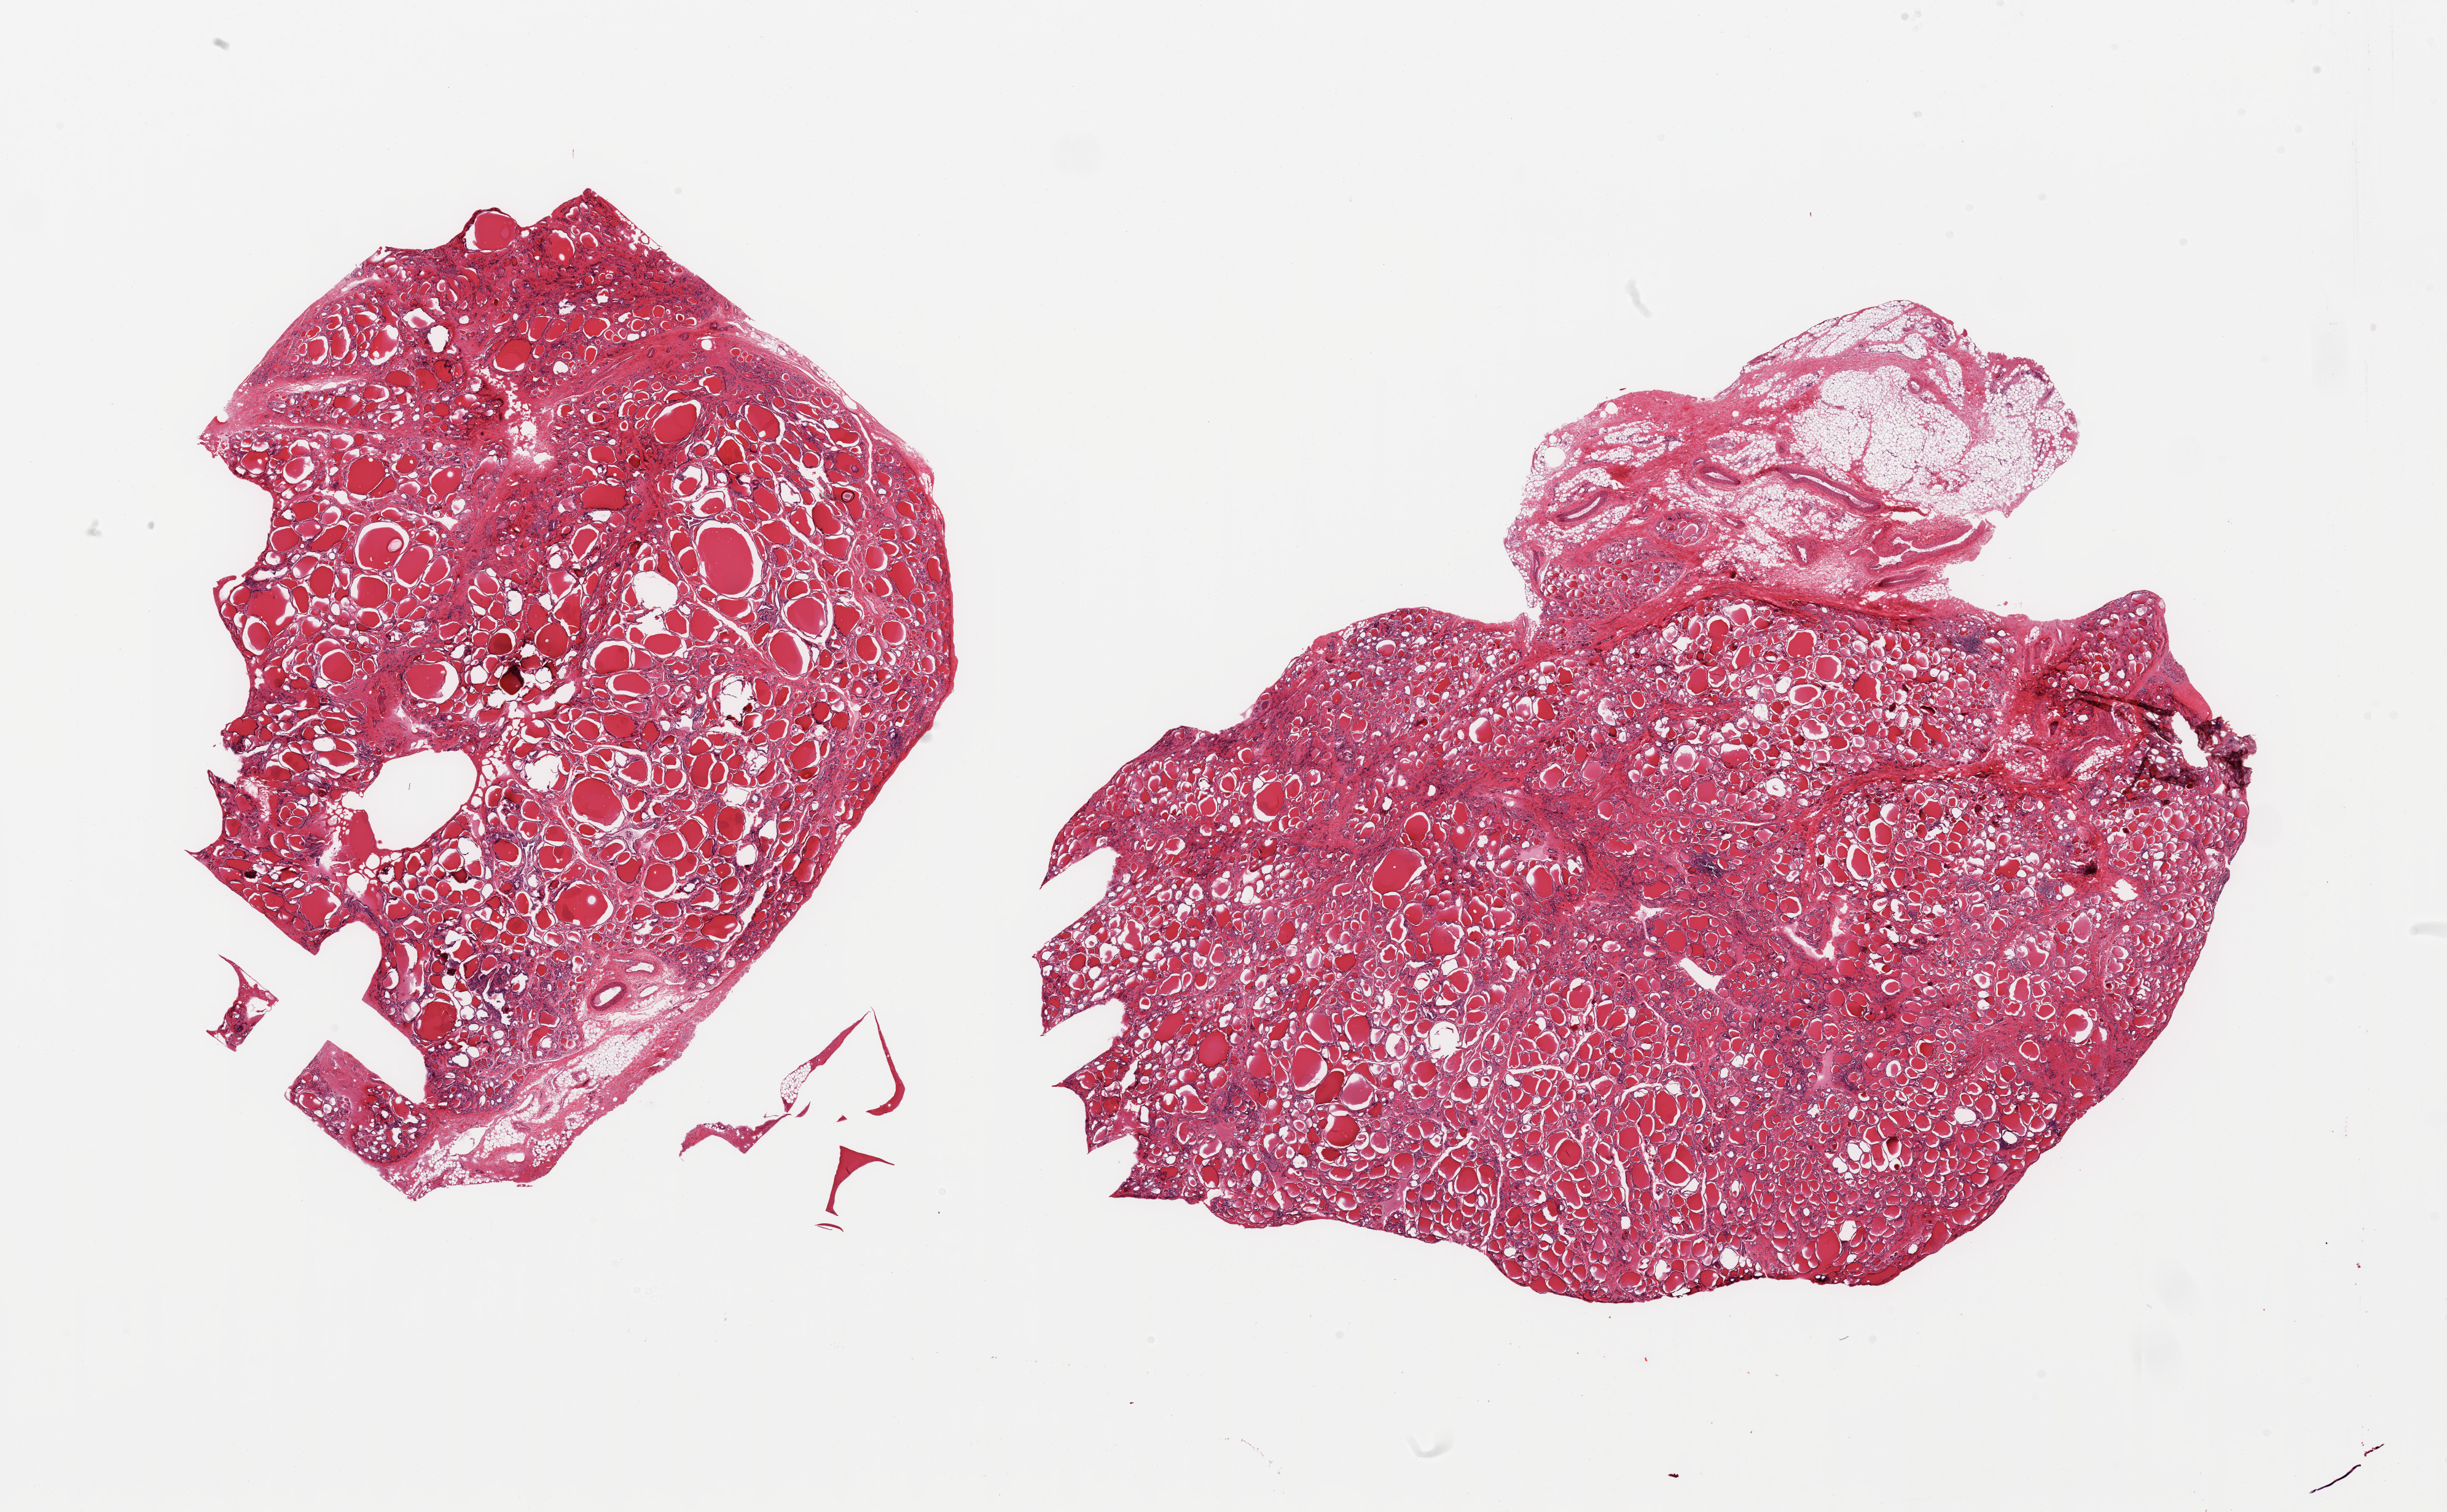
Whole-slide image, hematoxylin and eosin (H&E) stain, brightfield — low-resolution overview of the scanned area, about 31.5 x 19.5 mm; PAXgene-fixed paraffin-embedded (PFPE) section; section of thyroid (target tissue); tissue donor sample. Donor: male.
Review note (as recorded): 2 pieces; includes attachment of fat/vessels (5 and 15%); some interstitial fibrosis and few collections of lymphocytes.